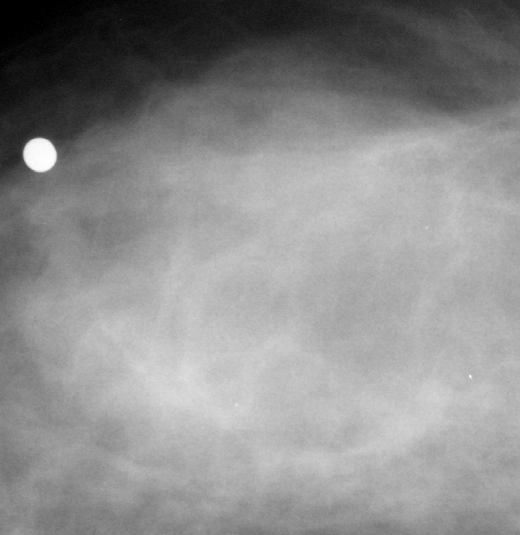
Cropped region of a digitized screen-film mammogram centred on a radiologist-marked abnormality, right breast, CC view.
Finding: mass, shape lobulated, margins obscured; BI-RADS assessment category 4; pathology result (as recorded, not read from the image): benign.